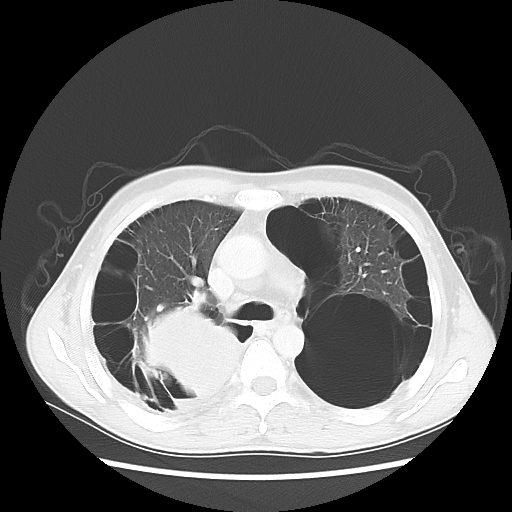
Chest CT, one axial slice; slice 37 of 57 in the series (ordered by position); lung window (W 1500 / L -600 HU); 5 mm slice thickness; 512 × 512 image matrix. Patient: male, 41 years. Case-level facts recorded for this patient, not image findings: clinical TNM (as recorded): T4 N0 M1a; histopathological grade: G3.
Structures marked on this image (rectangle marked by the reading radiologist):
- lung tumour (recorded histology: large cell carcinoma): box from (x=136, y=309) to (x=241, y=394) px